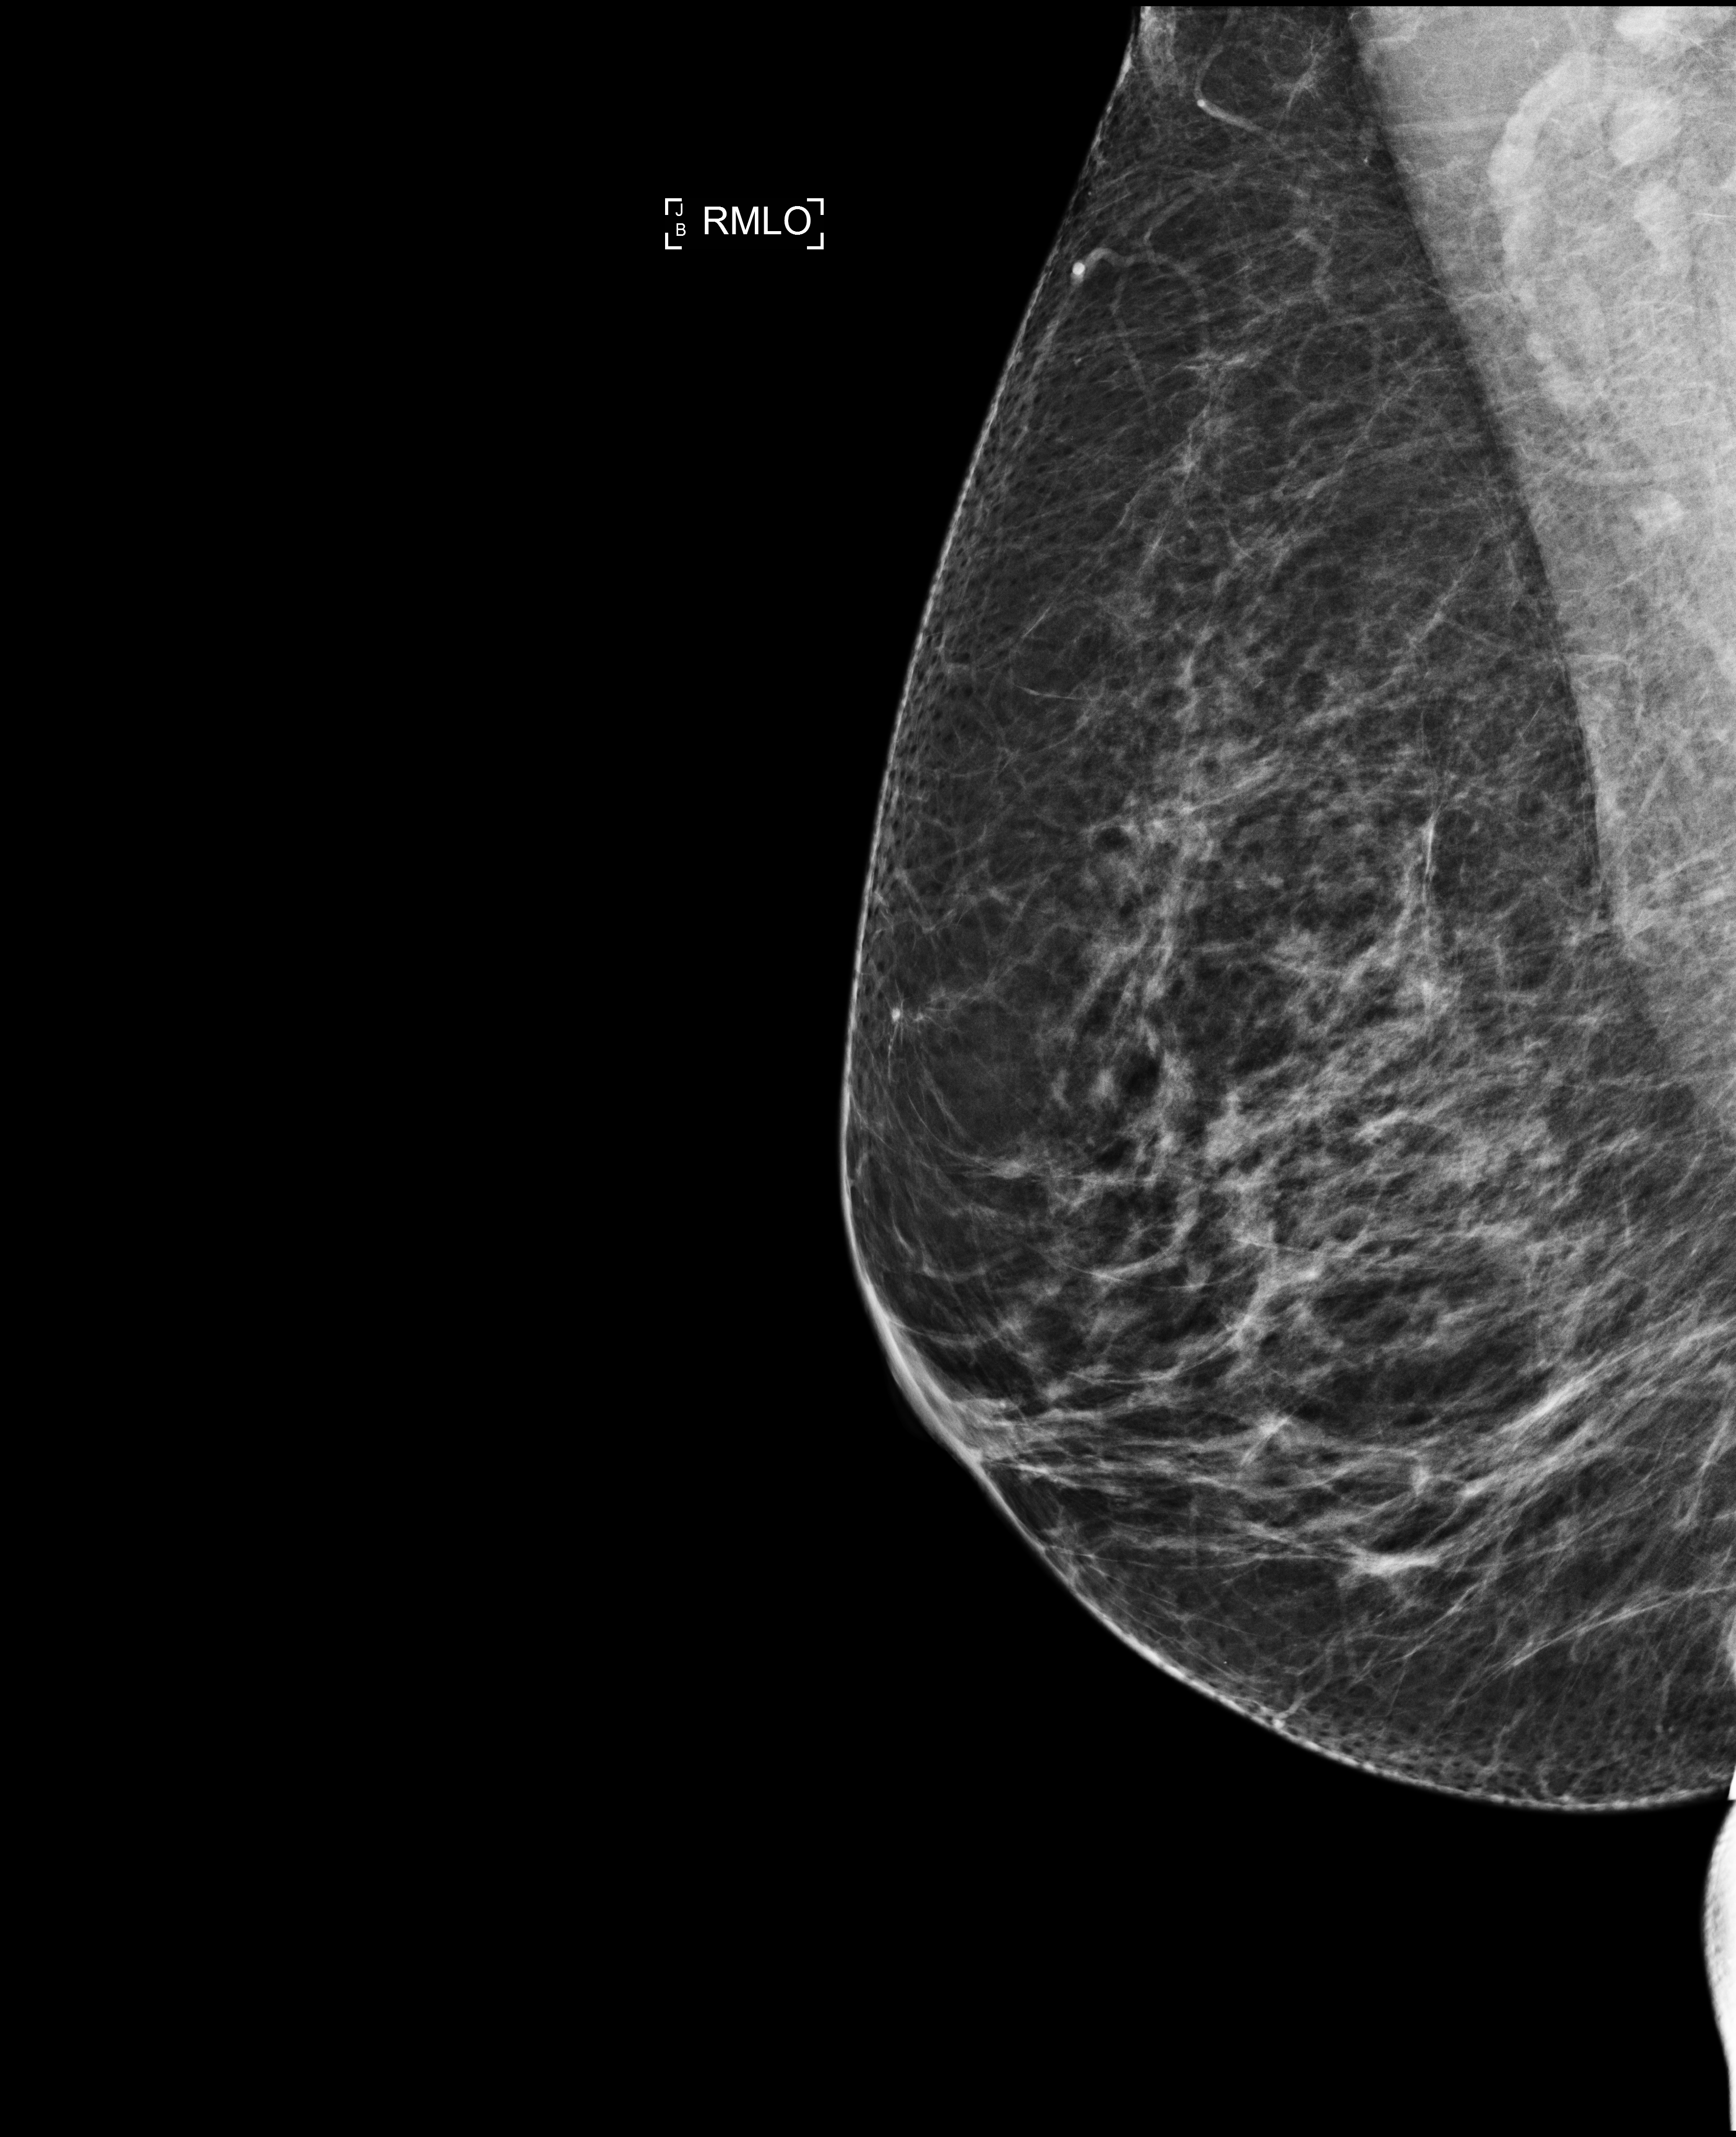
Digital mammogram (FFDM), right breast, MLO view, screening examination, compressed breast thickness 73 mm, system: Selenia Dimensions. Patient aged 62 years (female).
- BI-RADS breast density category at the screening exam (both breasts, scale 1–4): 2
- final BI-RADS assessment for this screening round (tomosynthesis exam, both breasts): category 2
- recall: recalled for additional imaging after this screen